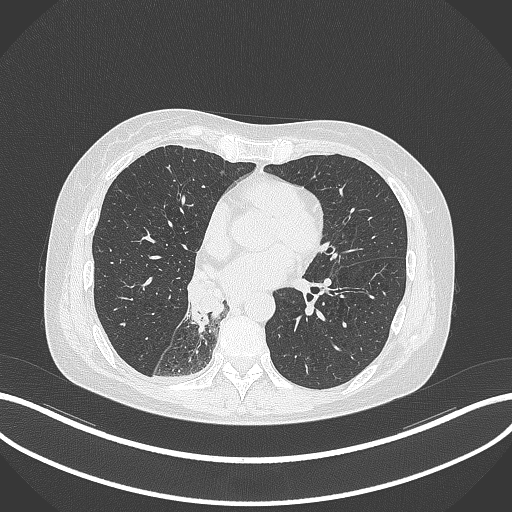
Chest CT, one axial slice; lung window (W 1500 / L -600 HU); 1 mm slice thickness; 512 × 512 image matrix, field of view 400 × 400 mm. Female patient, age 63 years. Case-level facts recorded for this patient, not image findings: clinical TNM (as recorded): T1c N0 M0.
Annotated regions visible in this slice (bounding box drawn by a radiologist):
- lung tumour (recorded histology: adenocarcinoma): bounding box <183,267,225,335> (left, top, right, bottom; pixels)